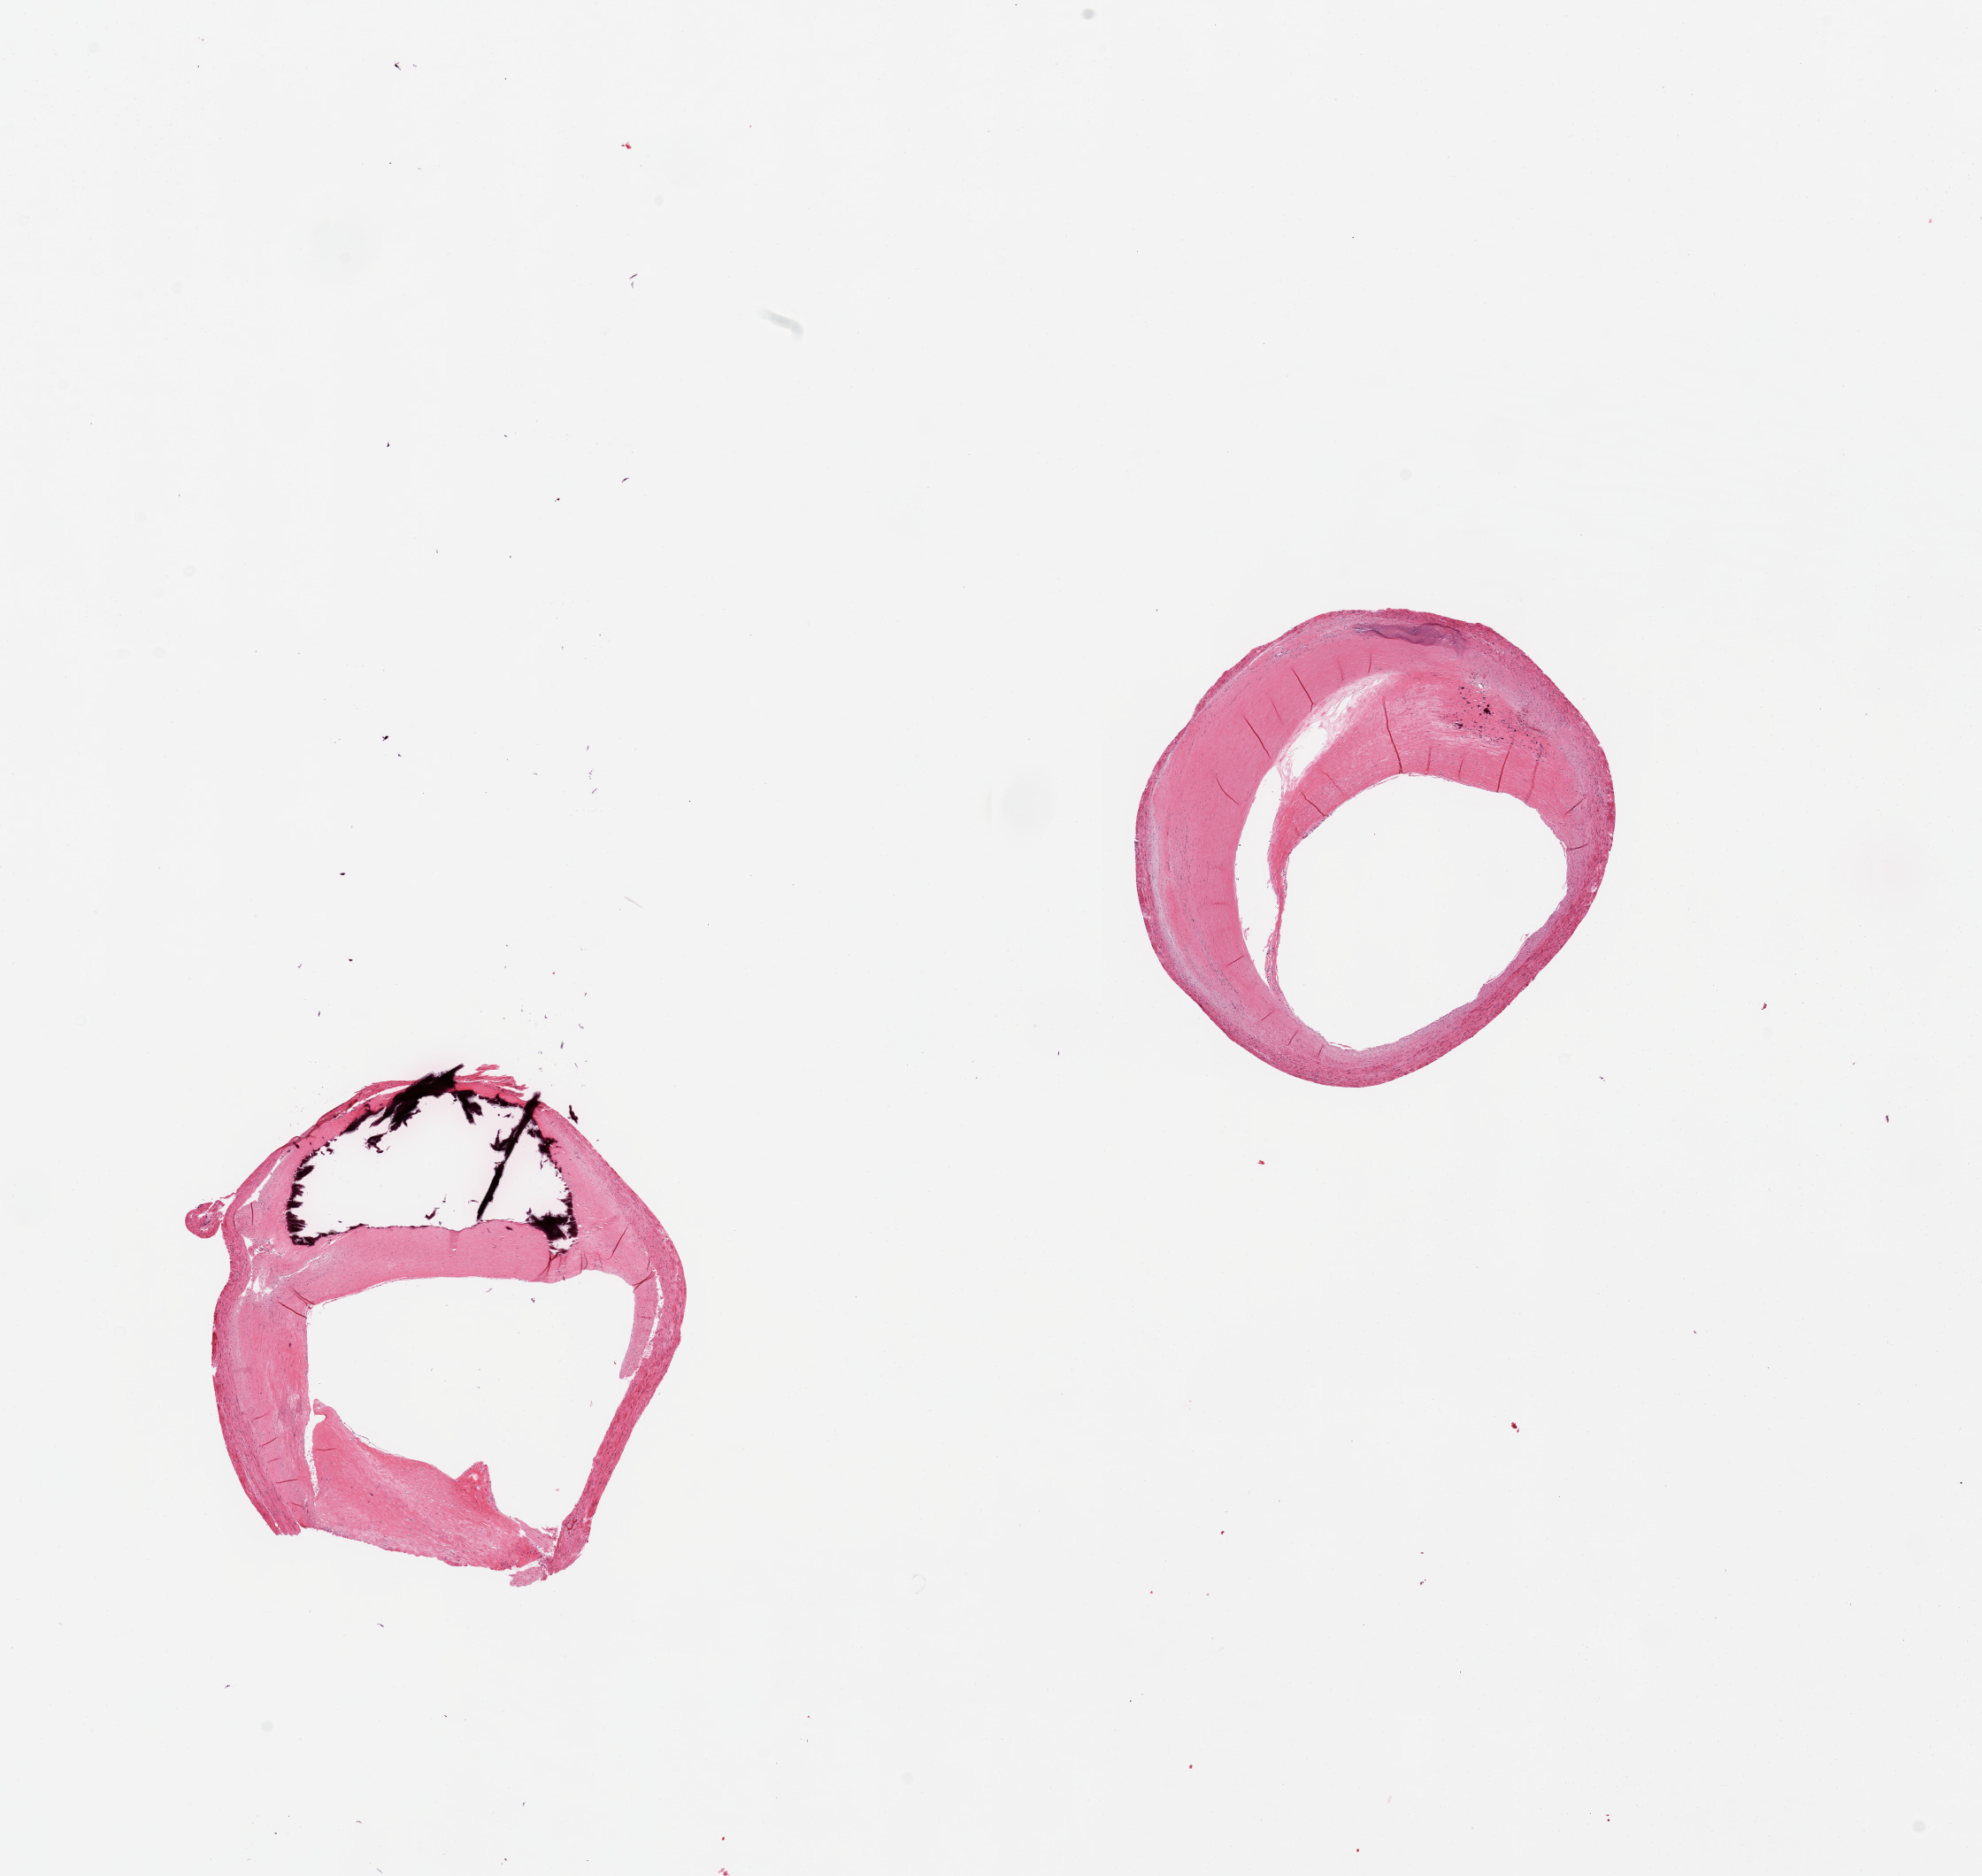
H&E whole-slide image, shown as a low-resolution overview of the whole scanned area (about 17.7 x 16.8 mm), PAXgene-fixed paraffin-embedded (PFPE) section, section of coronary artery (target tissue), donor tissue sample. Donor: male.
* reviewer comment on this tissue sample: 2 pieces; large (2 mm) eccentric calcified plaque